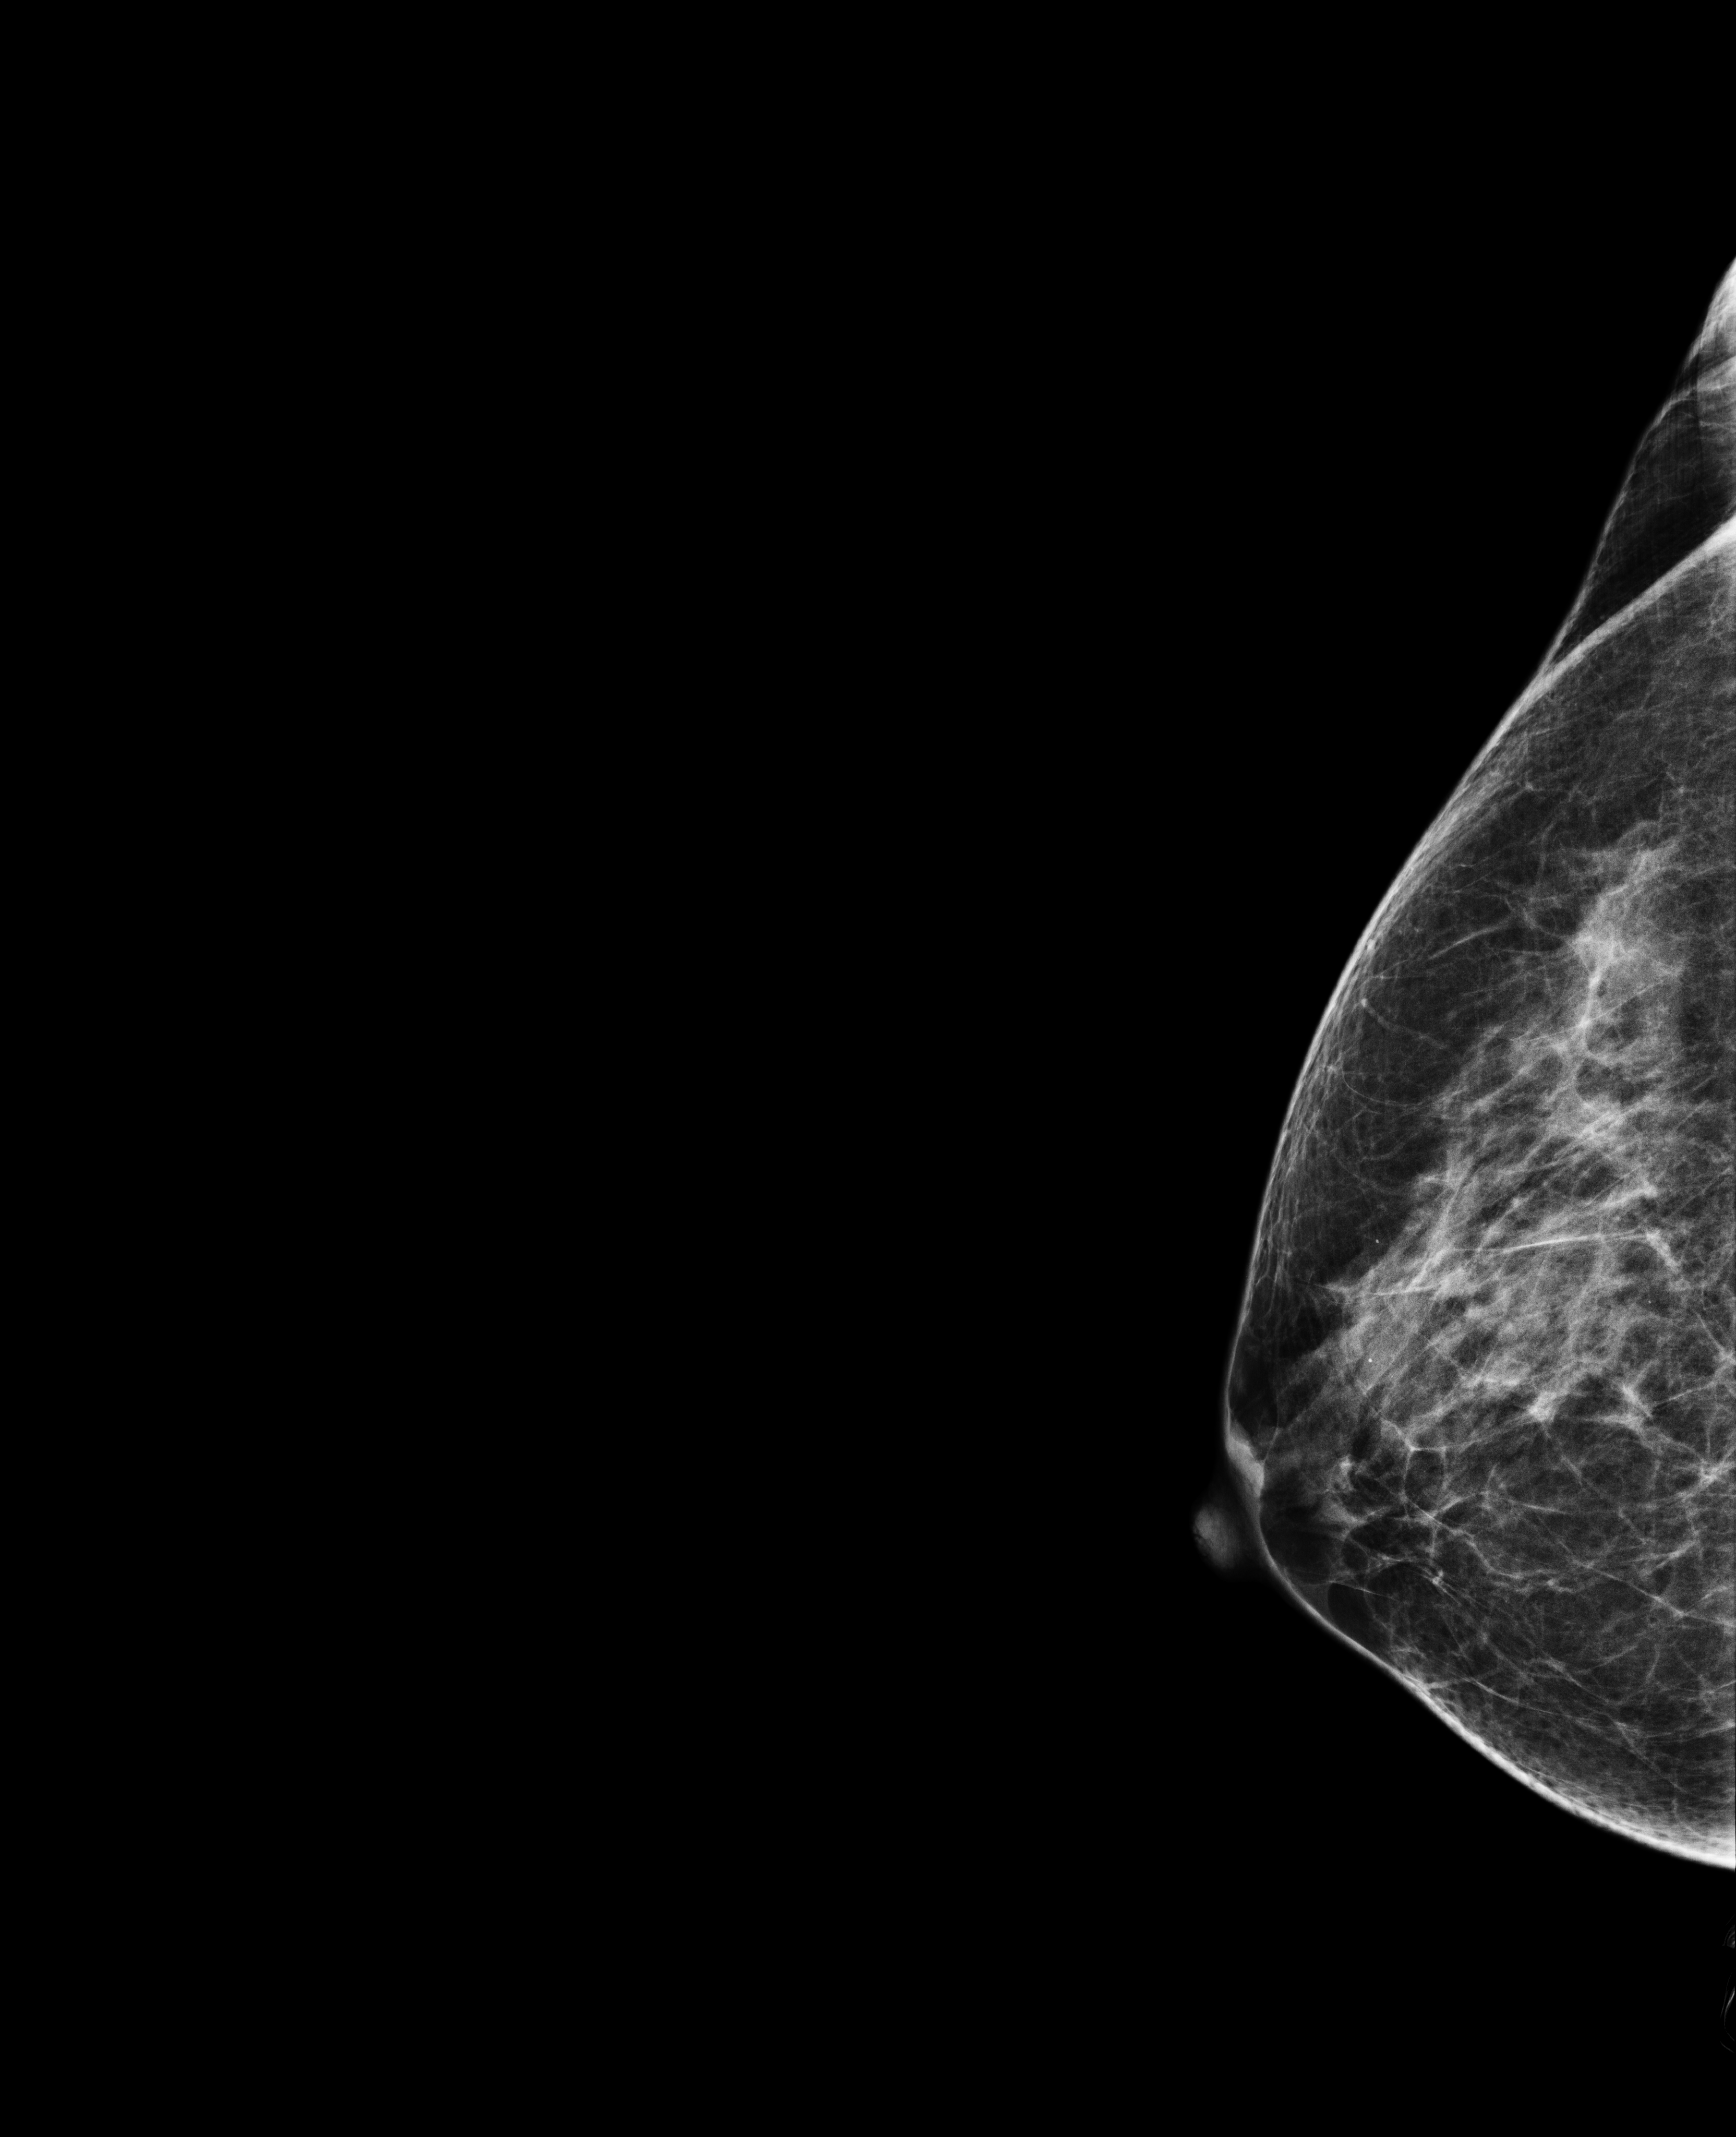
Annual screening mammography examination. Patient aged 50 years (female).
Image type: full-field digital mammogram. Breast: right. Projection: exaggerated CC view (lateral).